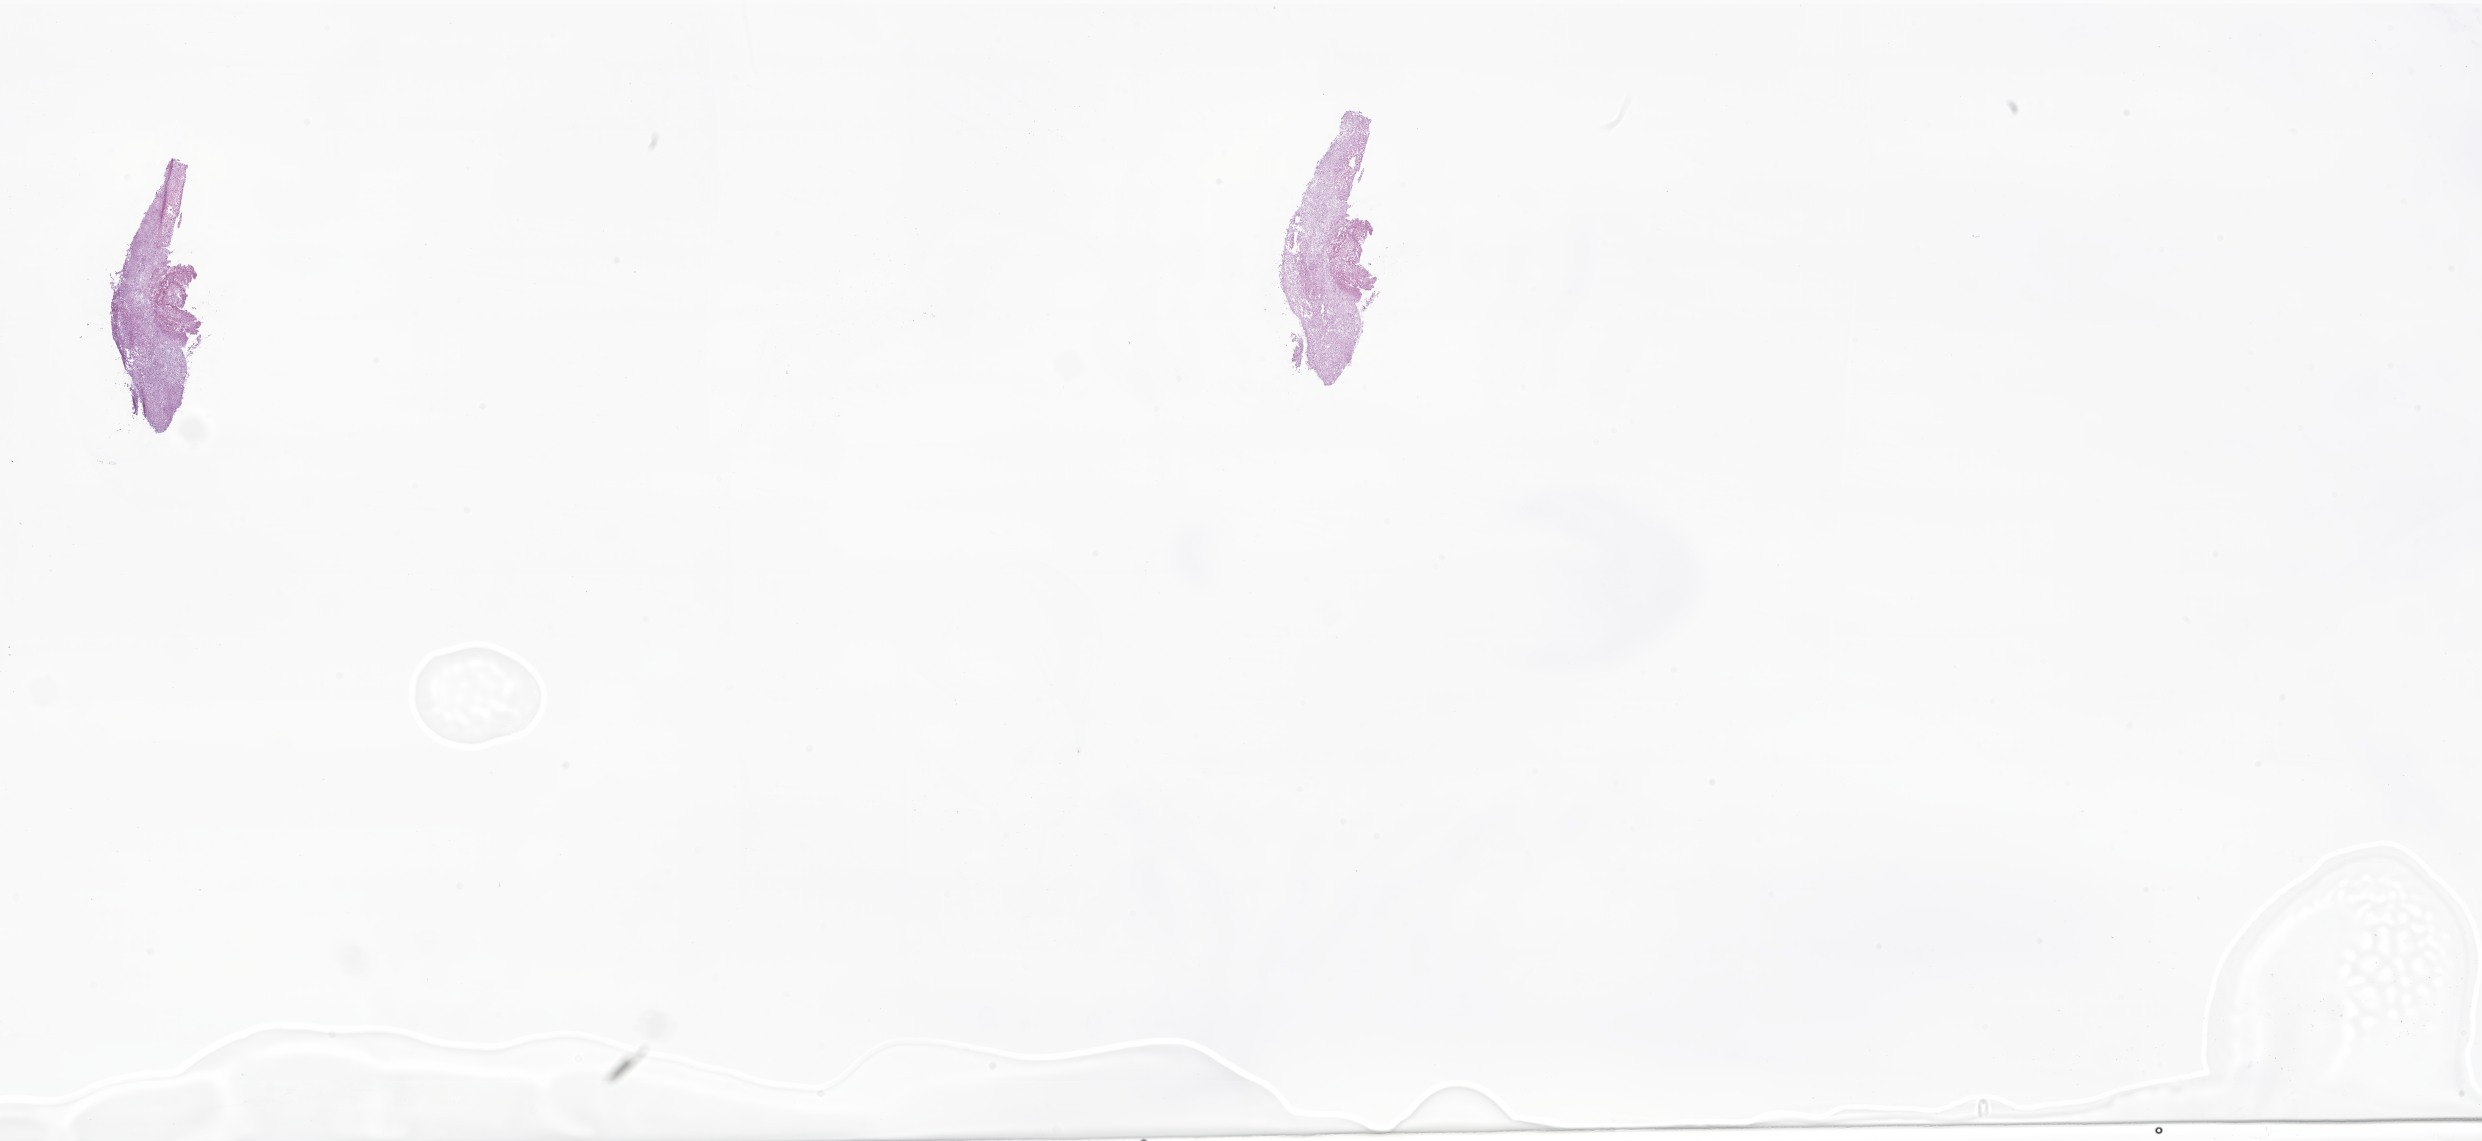
Whole-slide image, H&E stain of tumor tissue from the cerebellum — a low-resolution overview of the entire scanned area, about 41.9 x 19.2 mm, frozen section. Patient: female, age 210 months.
Diagnosis: Pilocytic astrocytoma.